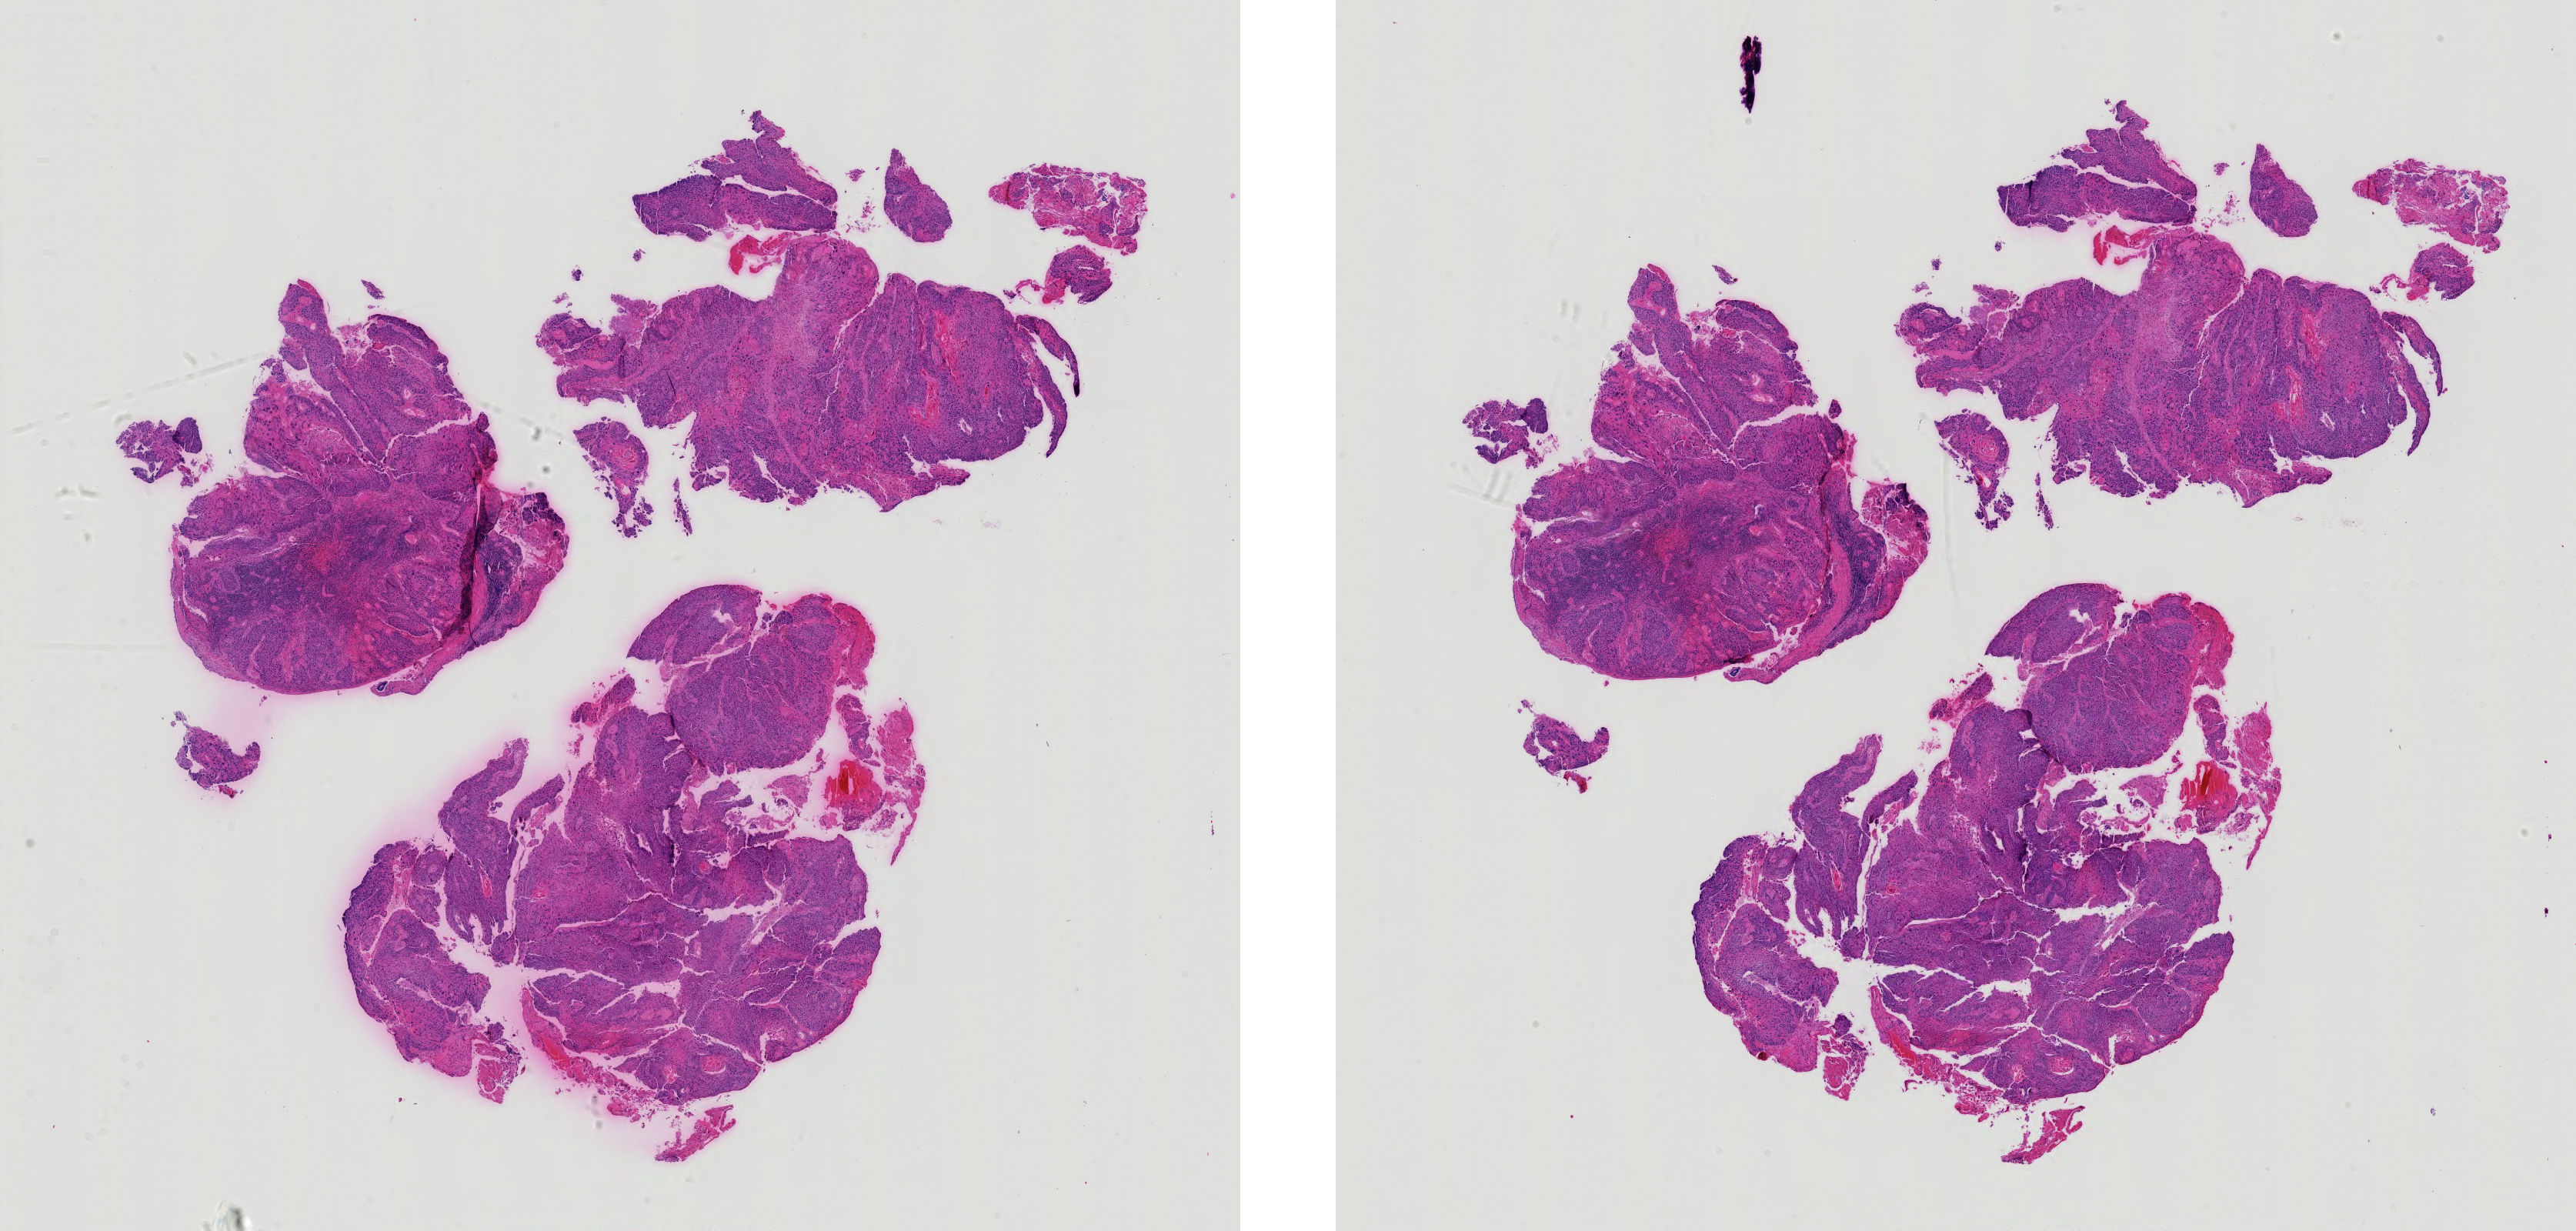
Digitized H&E-stained tissue section (whole slide) — low-resolution overview of the scanned area, about 24.3 x 11.6 mm; FFPE section; primary tumour sample from the head and neck. Male patient; age at initial diagnosis 60 years. Histologic grade: G2 (moderately differentiated).
Histologic diagnosis: Squamous cell carcinoma, NOS (oropharynx, NOS). Laterality: right.